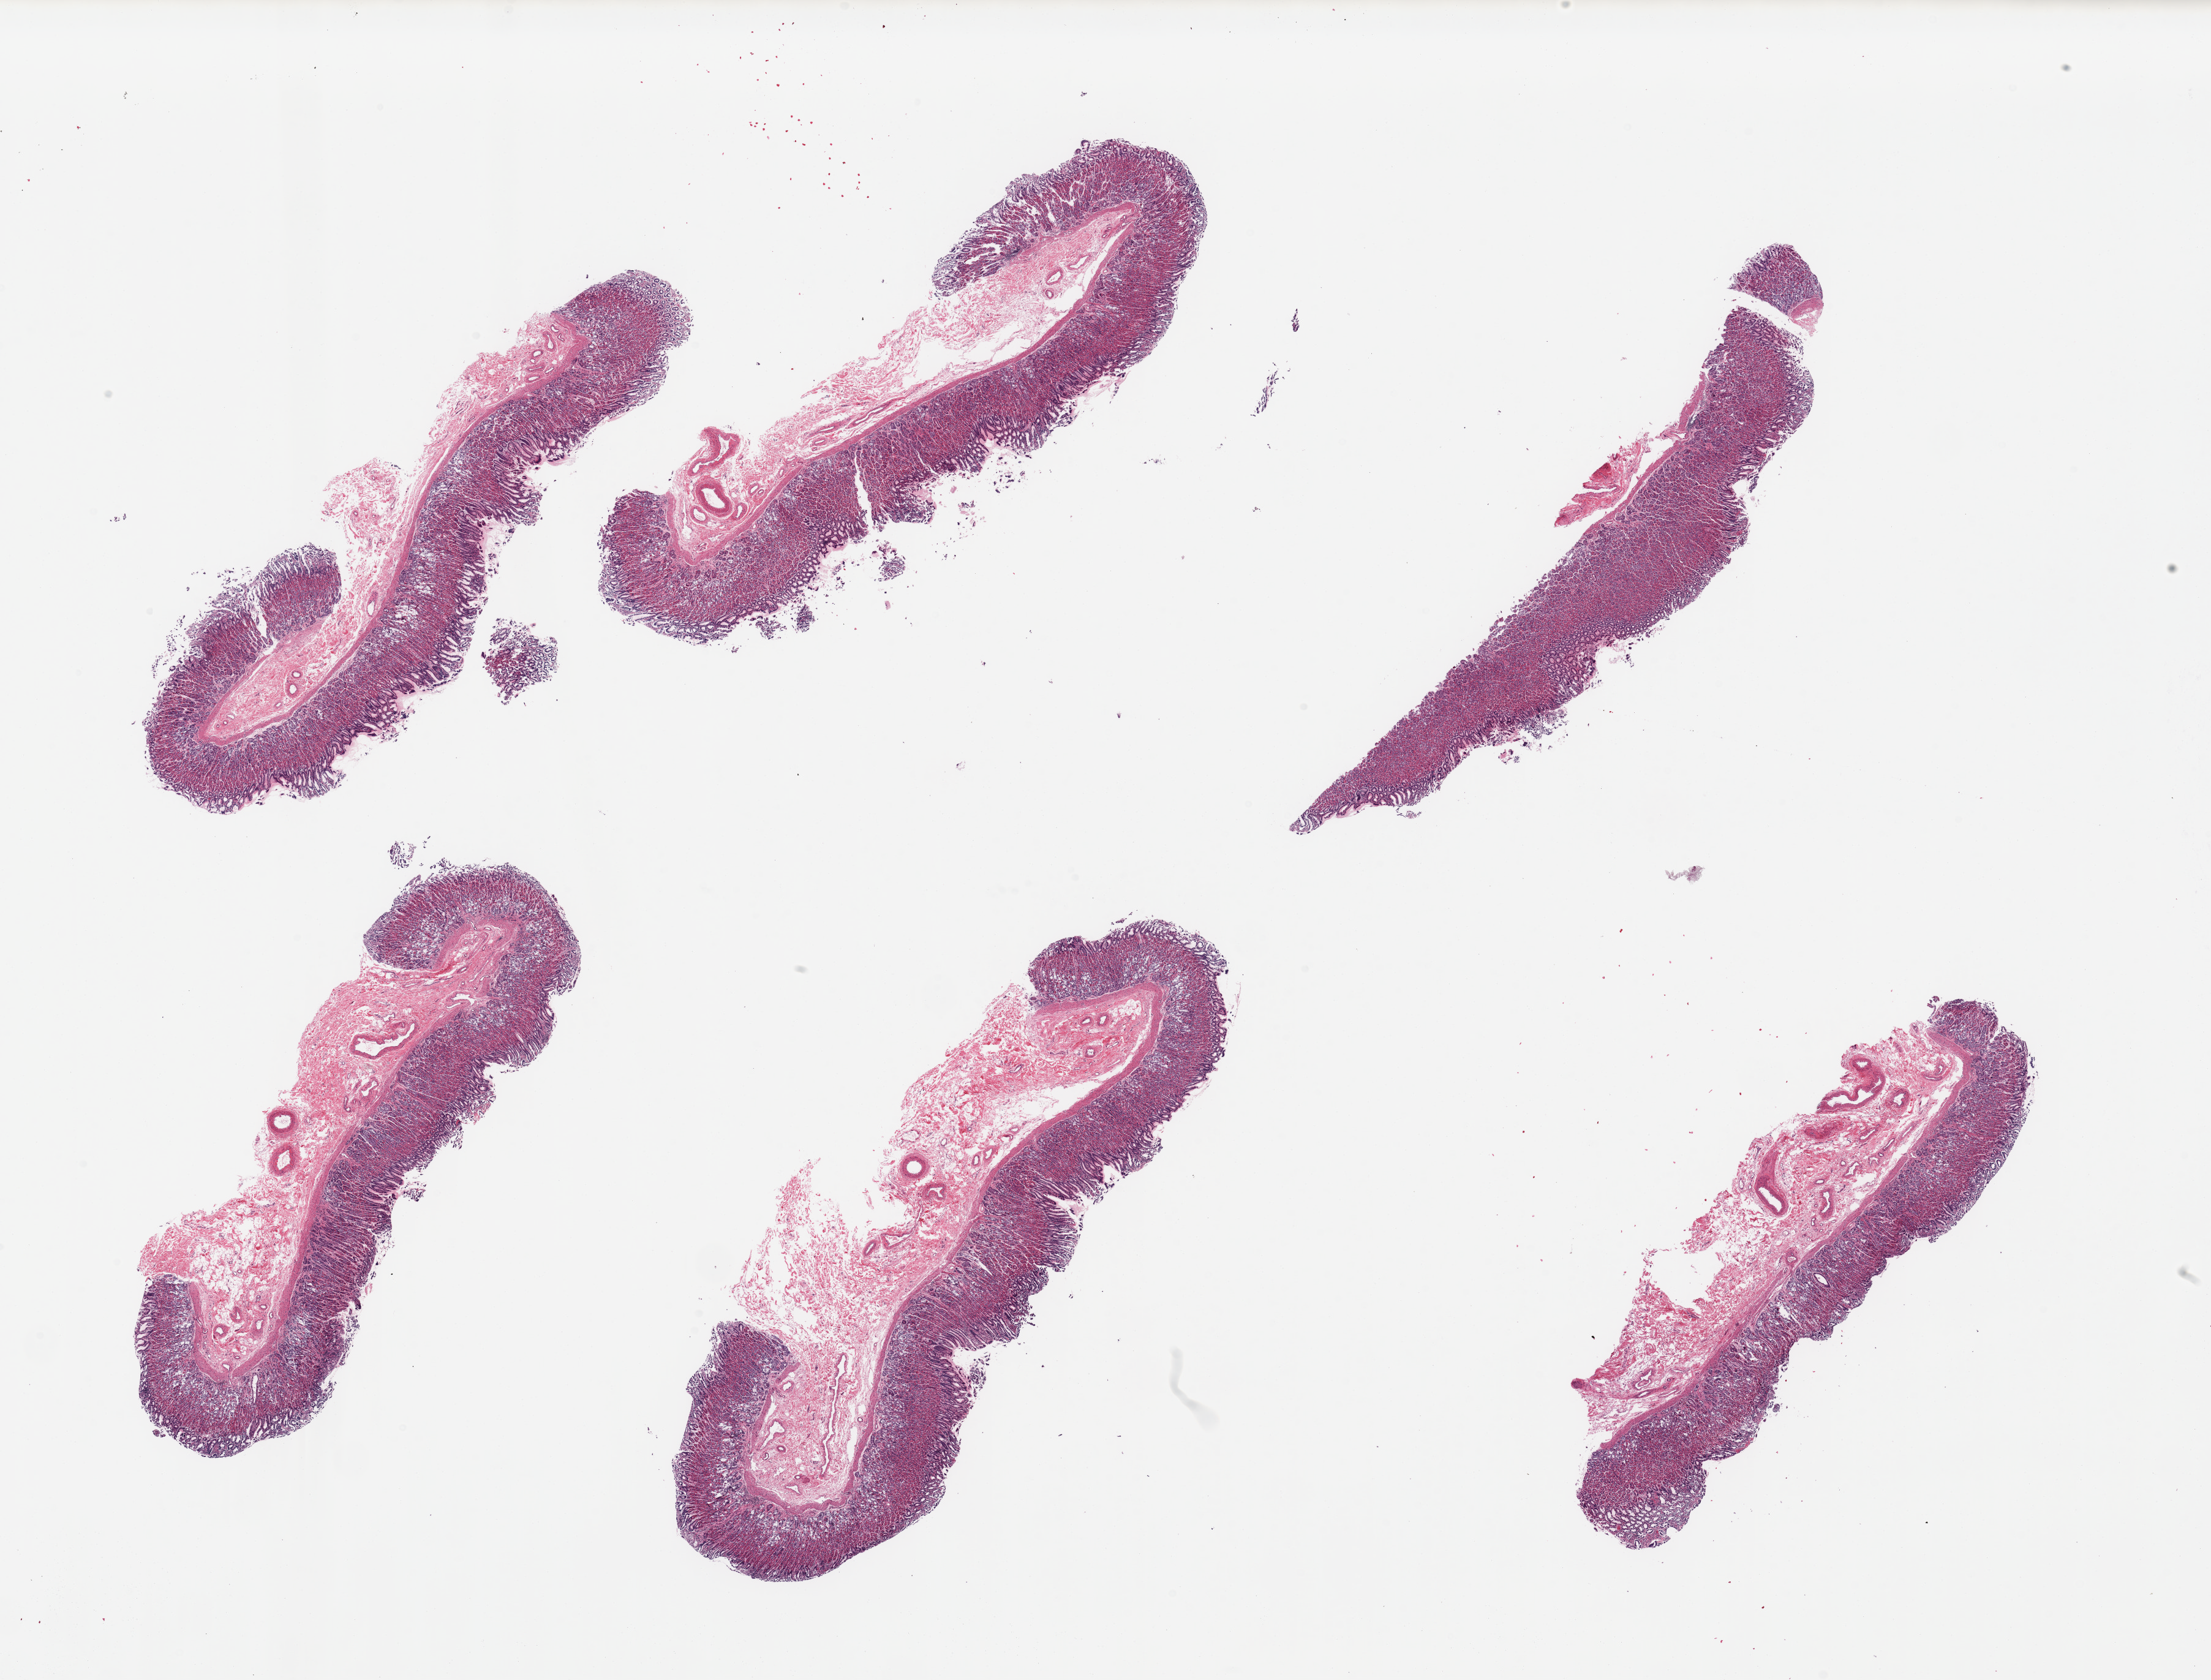
Digitized haematoxylin and eosin-stained section, brightfield, a low-resolution overview of the entire scanned area, about 28.5 x 21.7 mm, PAXgene-fixed paraffin-embedded (PFPE) section, section of stomach (target tissue), tissue donor sample. Donor: female.
Pathologist's review note for this sample: 6 pieces, mucosa up to ~1.2mm, ~40-60% thickness; Basal microglandular dilation, destruction of chief cells predominately, unusual pattern.